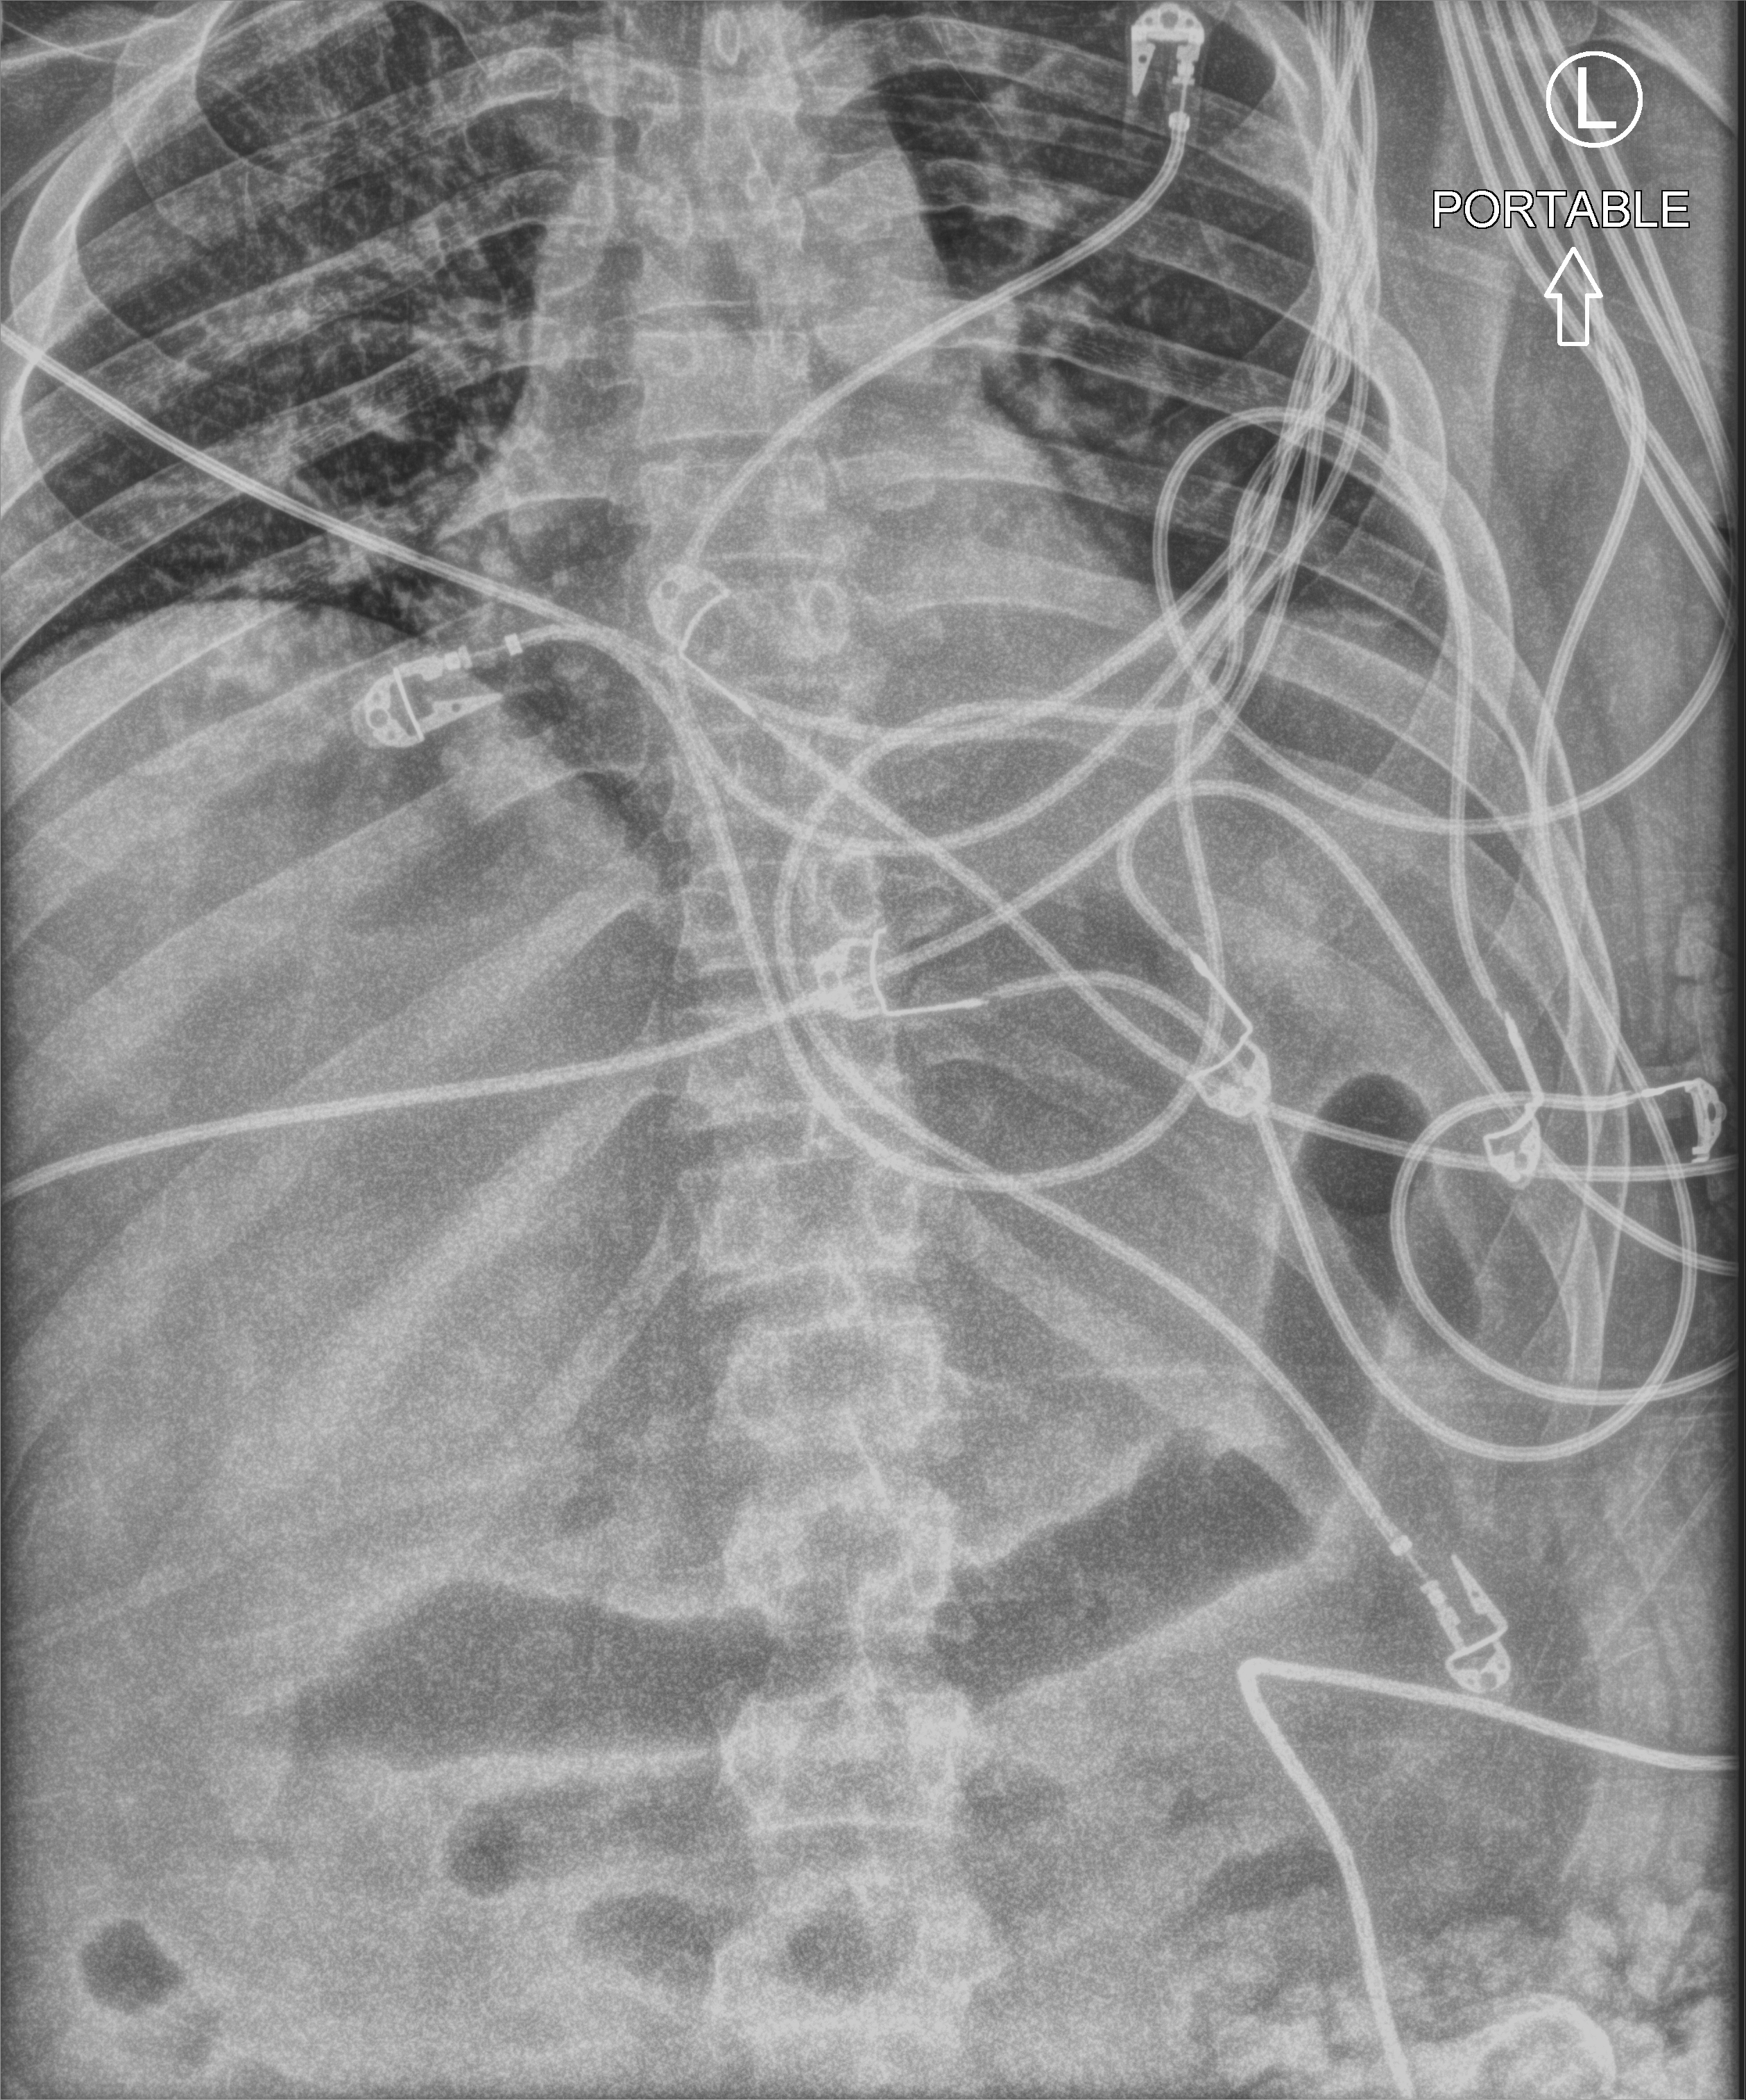
Portable abdomen radiograph, anteroposterior (AP) projection. Male patient hospitalised with COVID-19, age 18–59 years.
From the hospital-stay record, not from the radiograph (when in the stay this image was taken is not recorded): length of hospital stay: 61 days; other chronic lung disease (admission record): no.